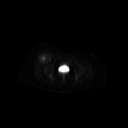
FDG PET of an extremity soft-tissue mass (from a PET/CT study), one axial slice; slice 65 of 267 in the series (ordered by position); 3.27 mm slice thickness; 128 × 128 image matrix, field of view 700 × 700 mm. Patient: female, 56 years. Case-level facts recorded for this patient, not image findings: histological type: malignant solitary fibrous tumor; grade: intermediate; site of the primary tumour: right thigh.
Outlined on this slice (expert contour drawn on MRI and transferred to this co-registered scan by the dataset authors):
- gross tumour volume including surrounding oedema: box from (x=36, y=54) to (x=49, y=62) px